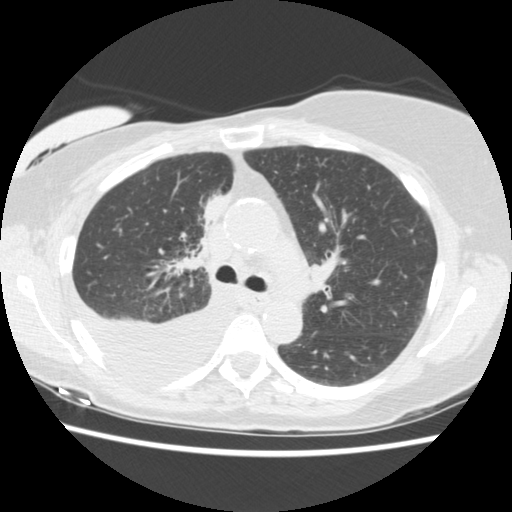
Low-dose screening chest CT, one axial slice. Position 98 of 157 along the scan axis. Reconstruction kernel STANDARD. Lung window (W 1500 / L -600 HU). 512 × 512 image matrix, field of view 330 × 330 mm.
Structures marked on this image (outlined manually by an expert reader):
- lesion 1 (tumor, upper lobe of right lung): bounding box (x1, y1, x2, y2) in pixels: (201, 196, 227, 225)